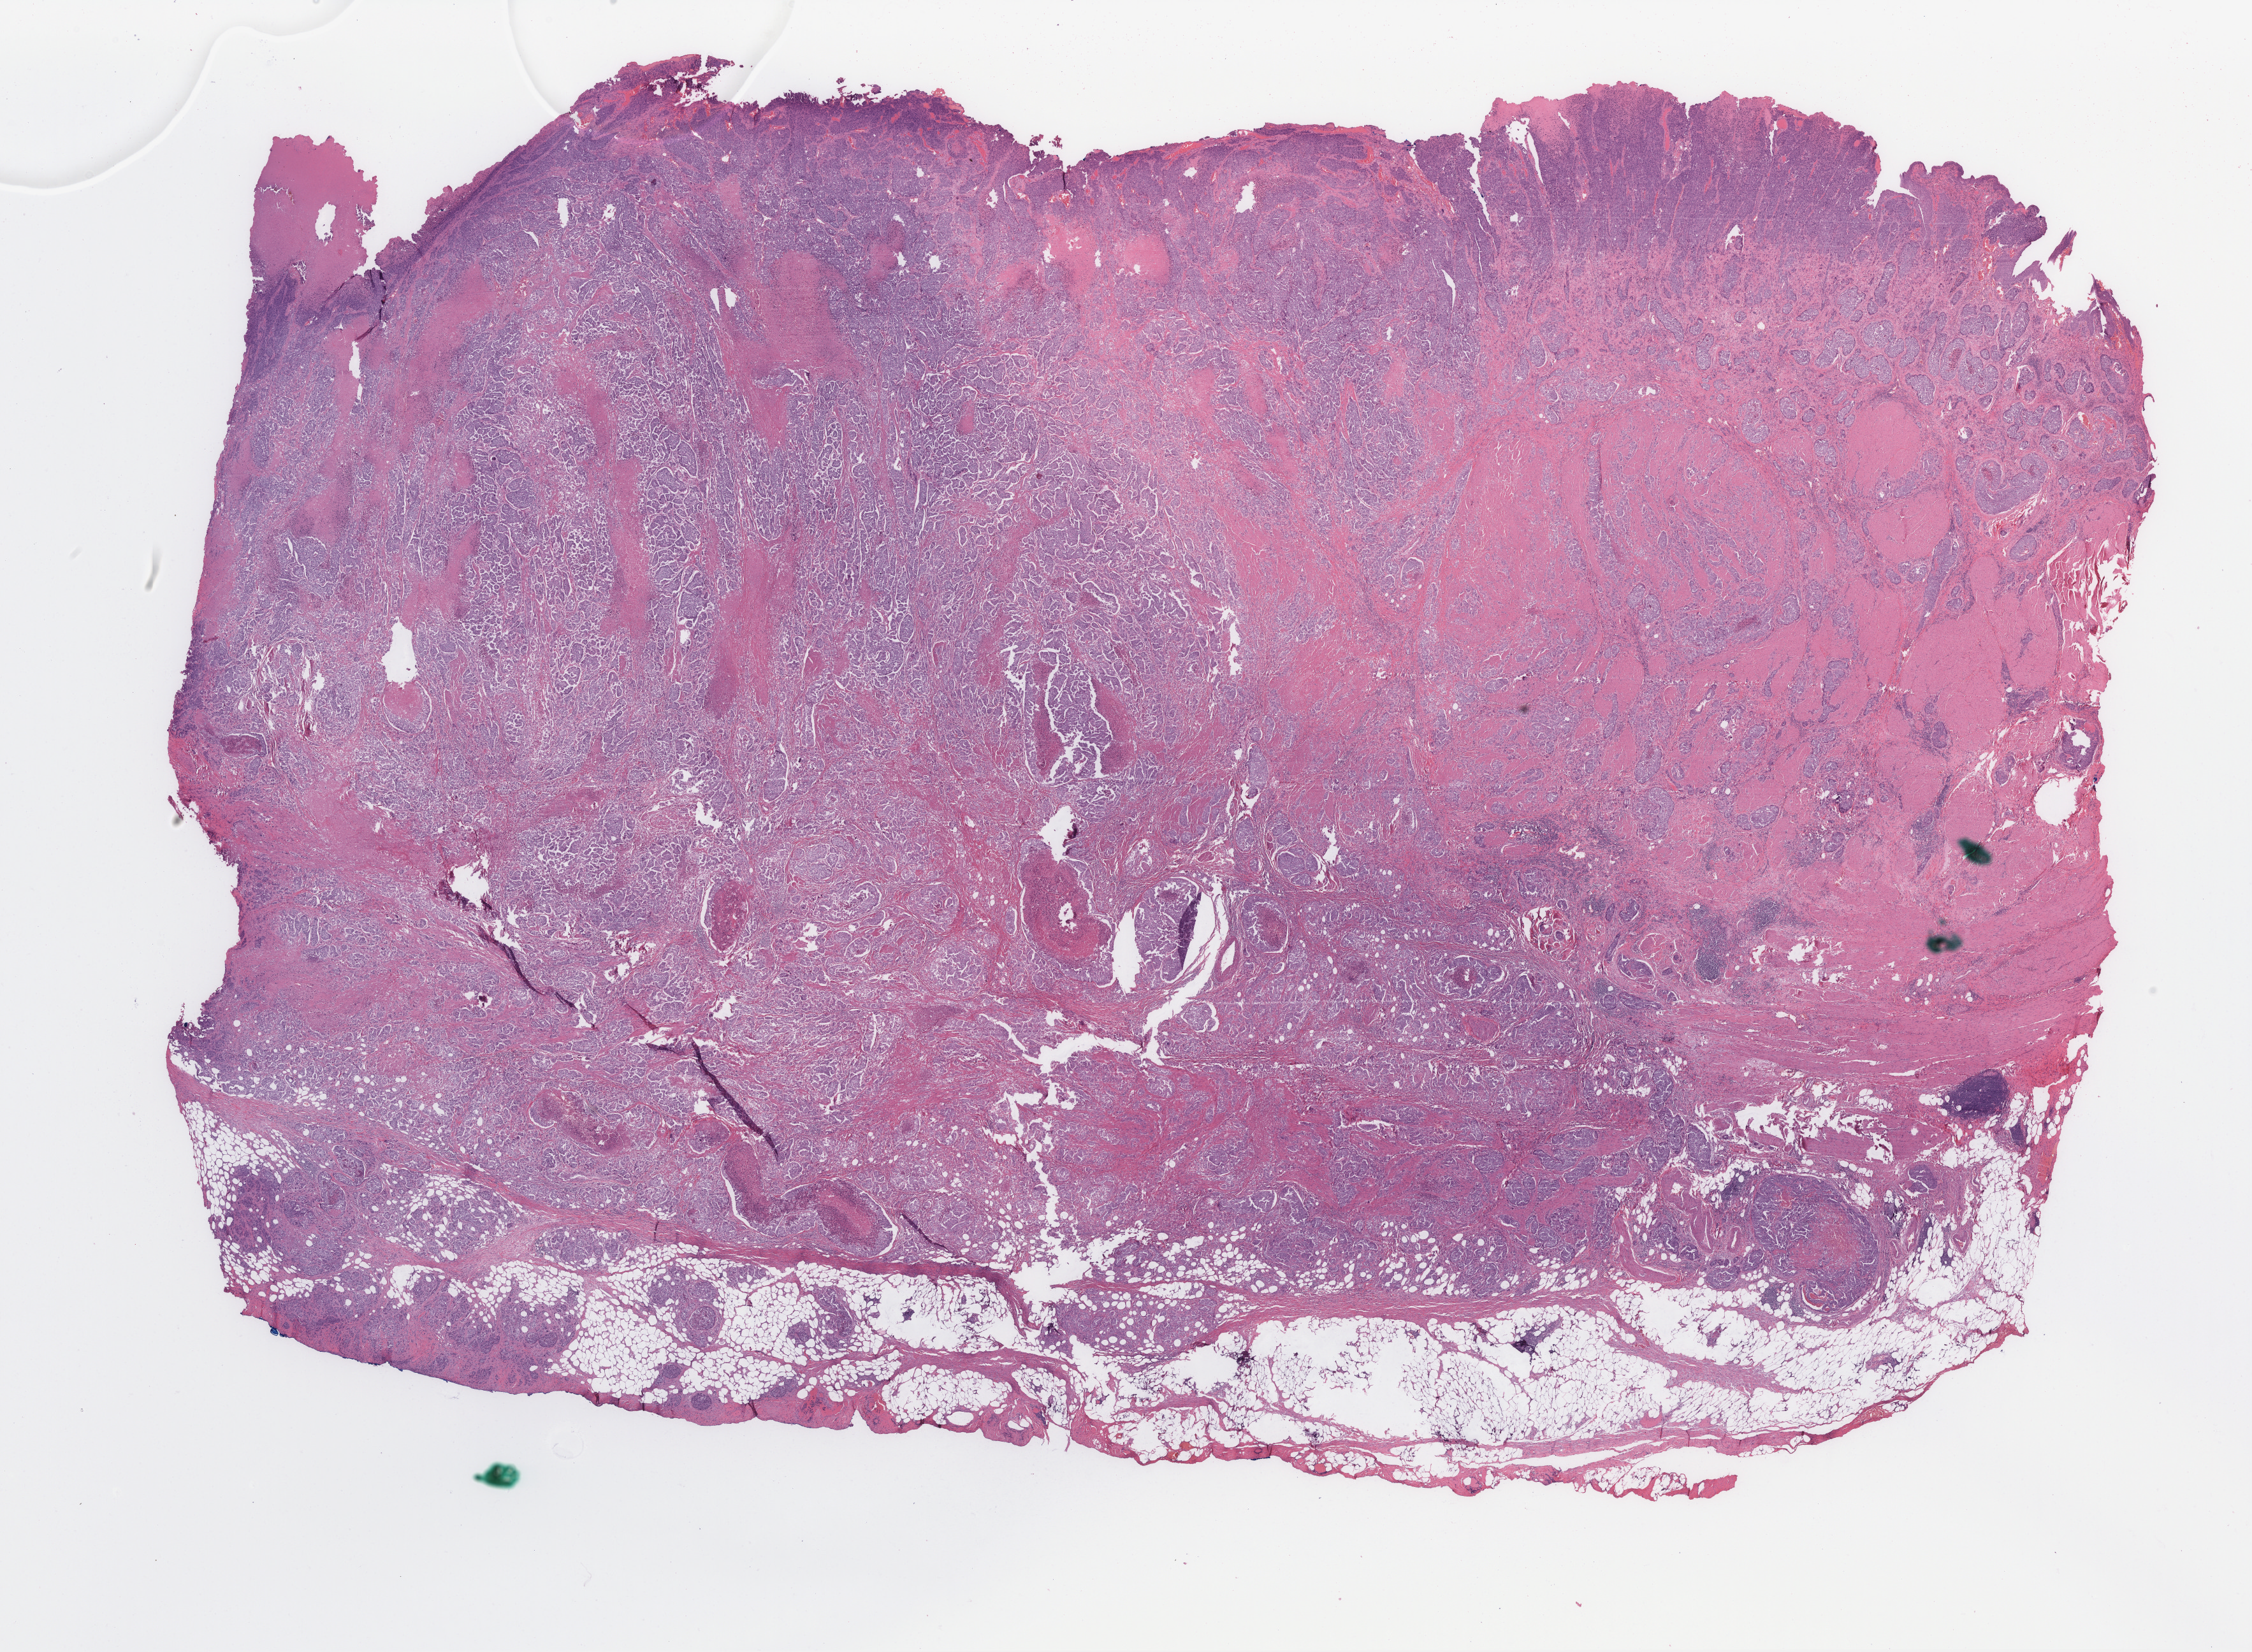
H&E-stained whole-slide image, shown as a low-resolution overview of the whole scanned area (about 28.0 x 20.6 mm, acquisition: 40x scan); FFPE section; sample: primary tumour, bladder. Male patient; age at initial diagnosis 65 years. Histologic grade: high grade.
- TNM: T3a N3 MX
- AJCC pathologic stage: IV (7th edition)
- lymph nodes positive (case pathology): 3 of 47 examined
- diagnosis: Transitional cell carcinoma (posterior wall of bladder)